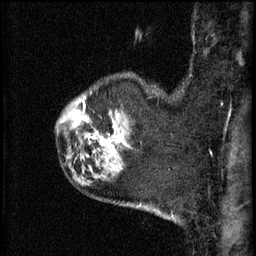
Breast MRI (dynamic contrast-enhanced), one sagittal slice. Slice 51 of 60 in the series (ordered by position). 3 images stored at this slice position (order not interpretable as contrast timing). 1.5 T. TE 4.2 ms, TR 11 ms. 2.3 mm slice thickness. 256 × 256 image matrix, field of view 180 × 180 mm. Female patient, age 52 years.
Annotated regions visible in this slice (semi-automatically segmented with operator editing):
- analysis volume of interest (the breast-tissue region the enhancement analysis was run in; not a lesion): bounding box <86,90,144,157> (left, top, right, bottom; pixels)
- tumour enhancement mask (voxels above the 70 % enhancement threshold inside the analysis volume of interest): <100,138,104,143>